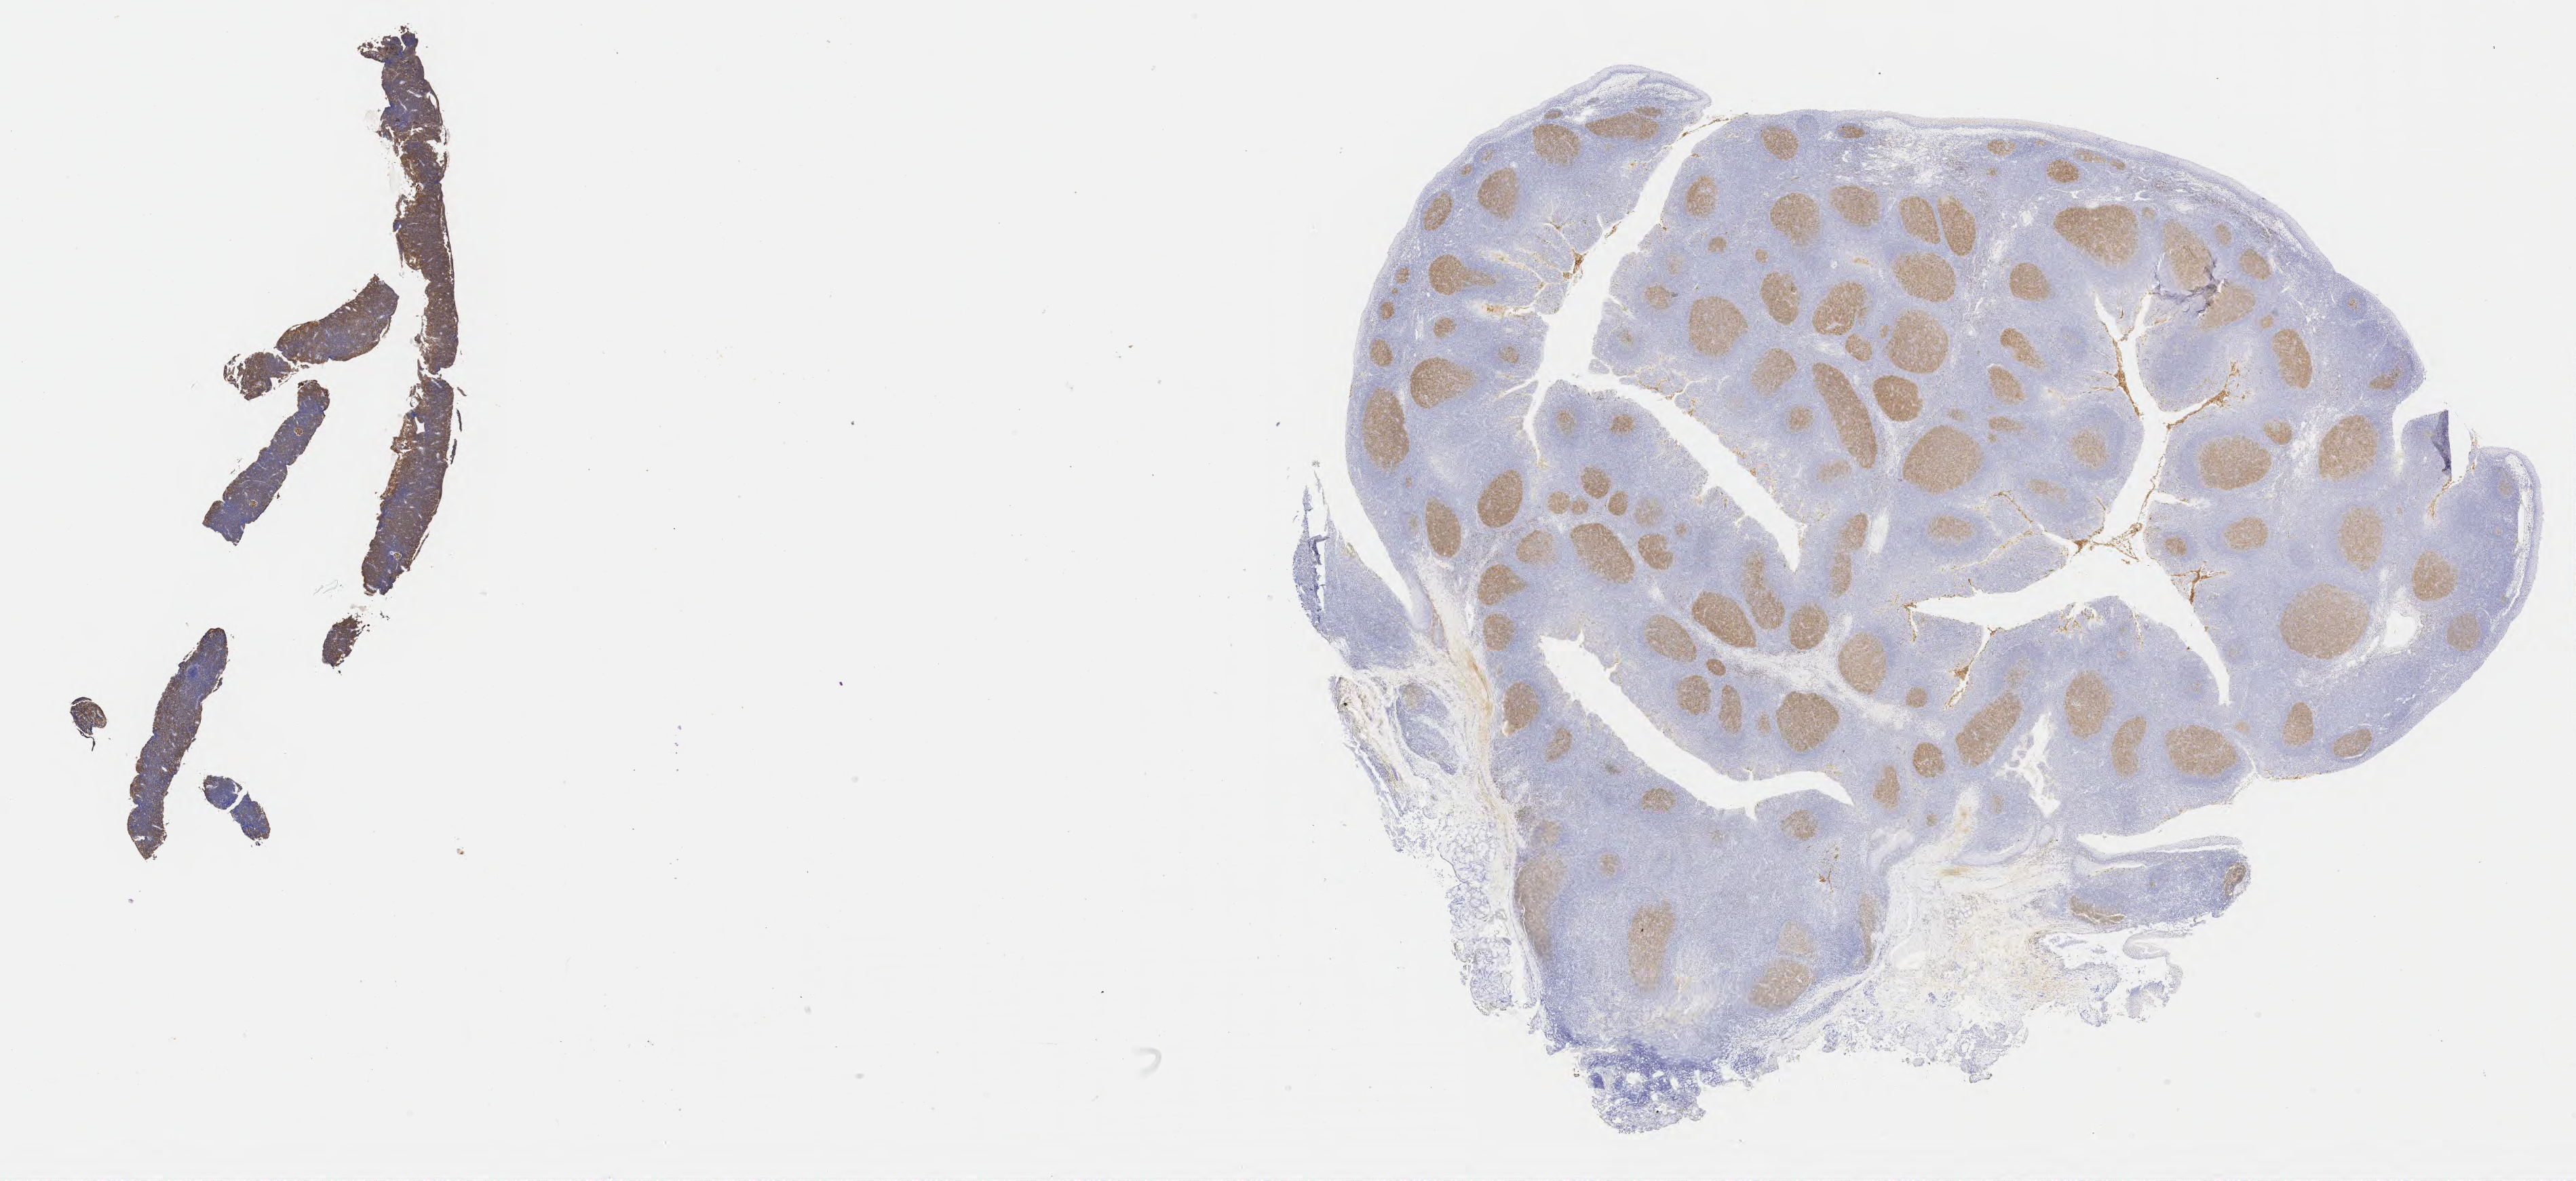
Immunohistochemistry (IHC) whole-slide image stained for CD10 — whole scanned area (about 30.7 x 14.1 mm) shown as a low-resolution overview; specimen: tumor tissue. Male patient; age at initial diagnosis 8 years.
• diagnosis: Burkitt lymphoma, NOS